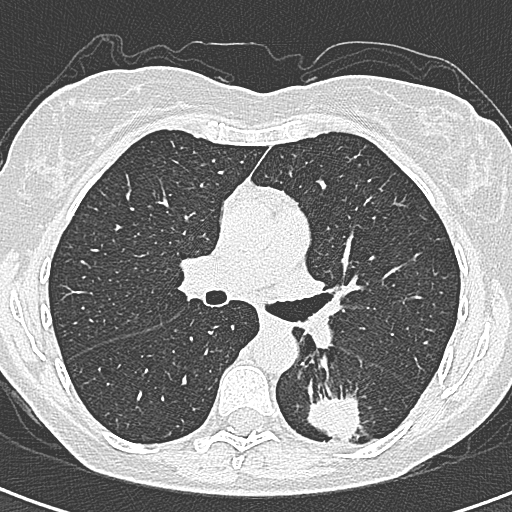
Low-dose screening chest CT, axial slice; baseline annual screen; lung window (W 1500 / L -600 HU); 1 mm slice thickness; slice 129 of 328 in the series. Female participant, aged 58 years at enrolment.
Lesion marked by an expert reader, bounding box (x1, y1, x2, y2) in pixels: (295, 388, 365, 455). The screening reader recorded 2 non-calcified nodules or masses ≥4 mm on this exam (left lower lobe, right lower lobe); which of them this box marks is not recorded. Official screen result: positive, change unspecified: nodule(s) >= 4 mm or enlarging nodule(s), mass(es), or other non-specific abnormalities suspicious for lung cancer. Later outcome: lung cancer diagnosed 22 days after this screen — adenocarcinoma, NOS, left lower lobe, moderately differentiated (G2), stage IA (AJCC 6th edition), 25 mm at pathology.